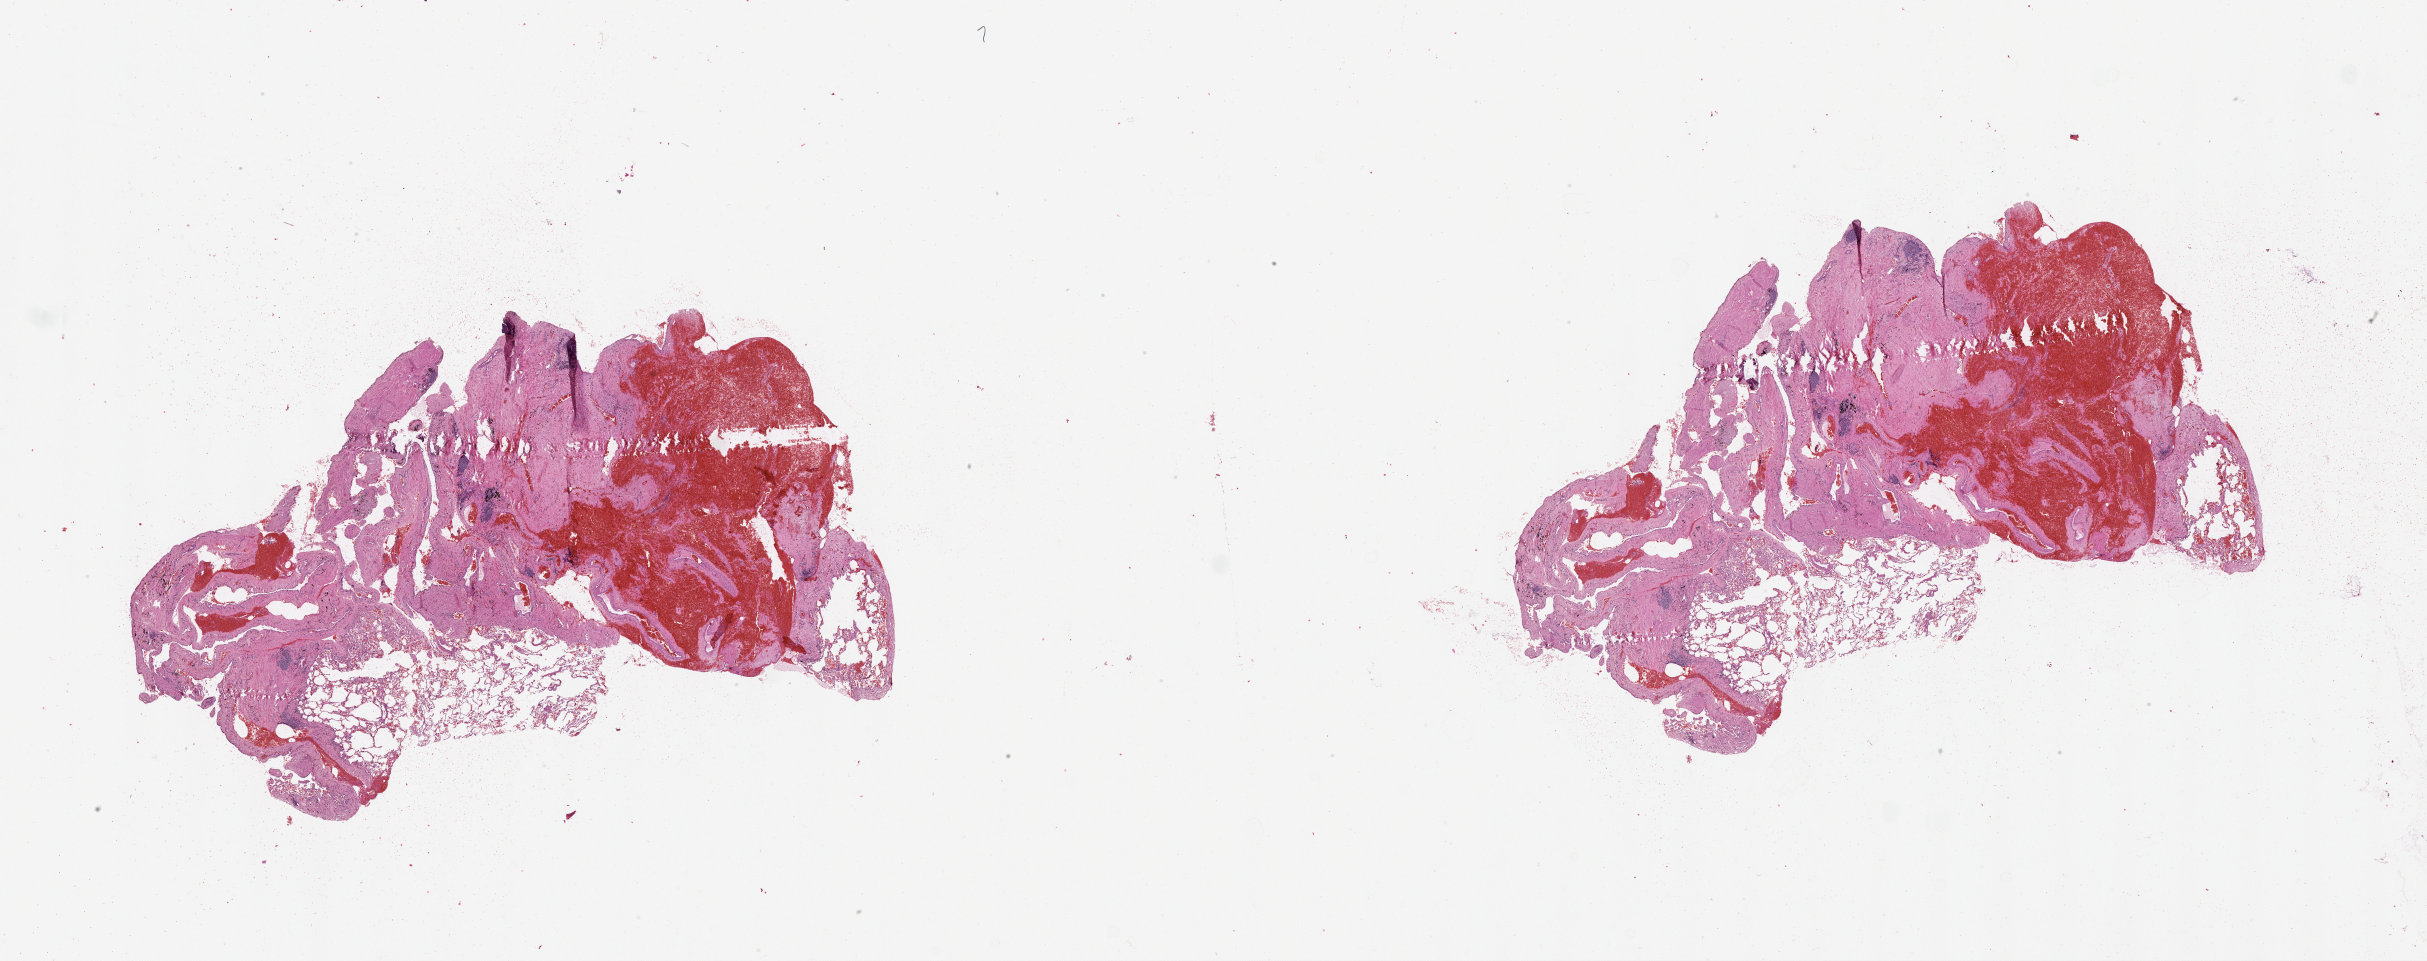
Hematoxylin and eosin (H&E) stained whole-slide image — whole scanned area (about 39.1 x 15.5 mm) shown as a low-resolution overview. Normal (non-tumour) tissue sample, lung. Male, 59 y/o.
This section: normal (non-tumour) tissue from the same patient. Patient diagnosis (cohort enrolment): squamous cell carcinoma (lung).